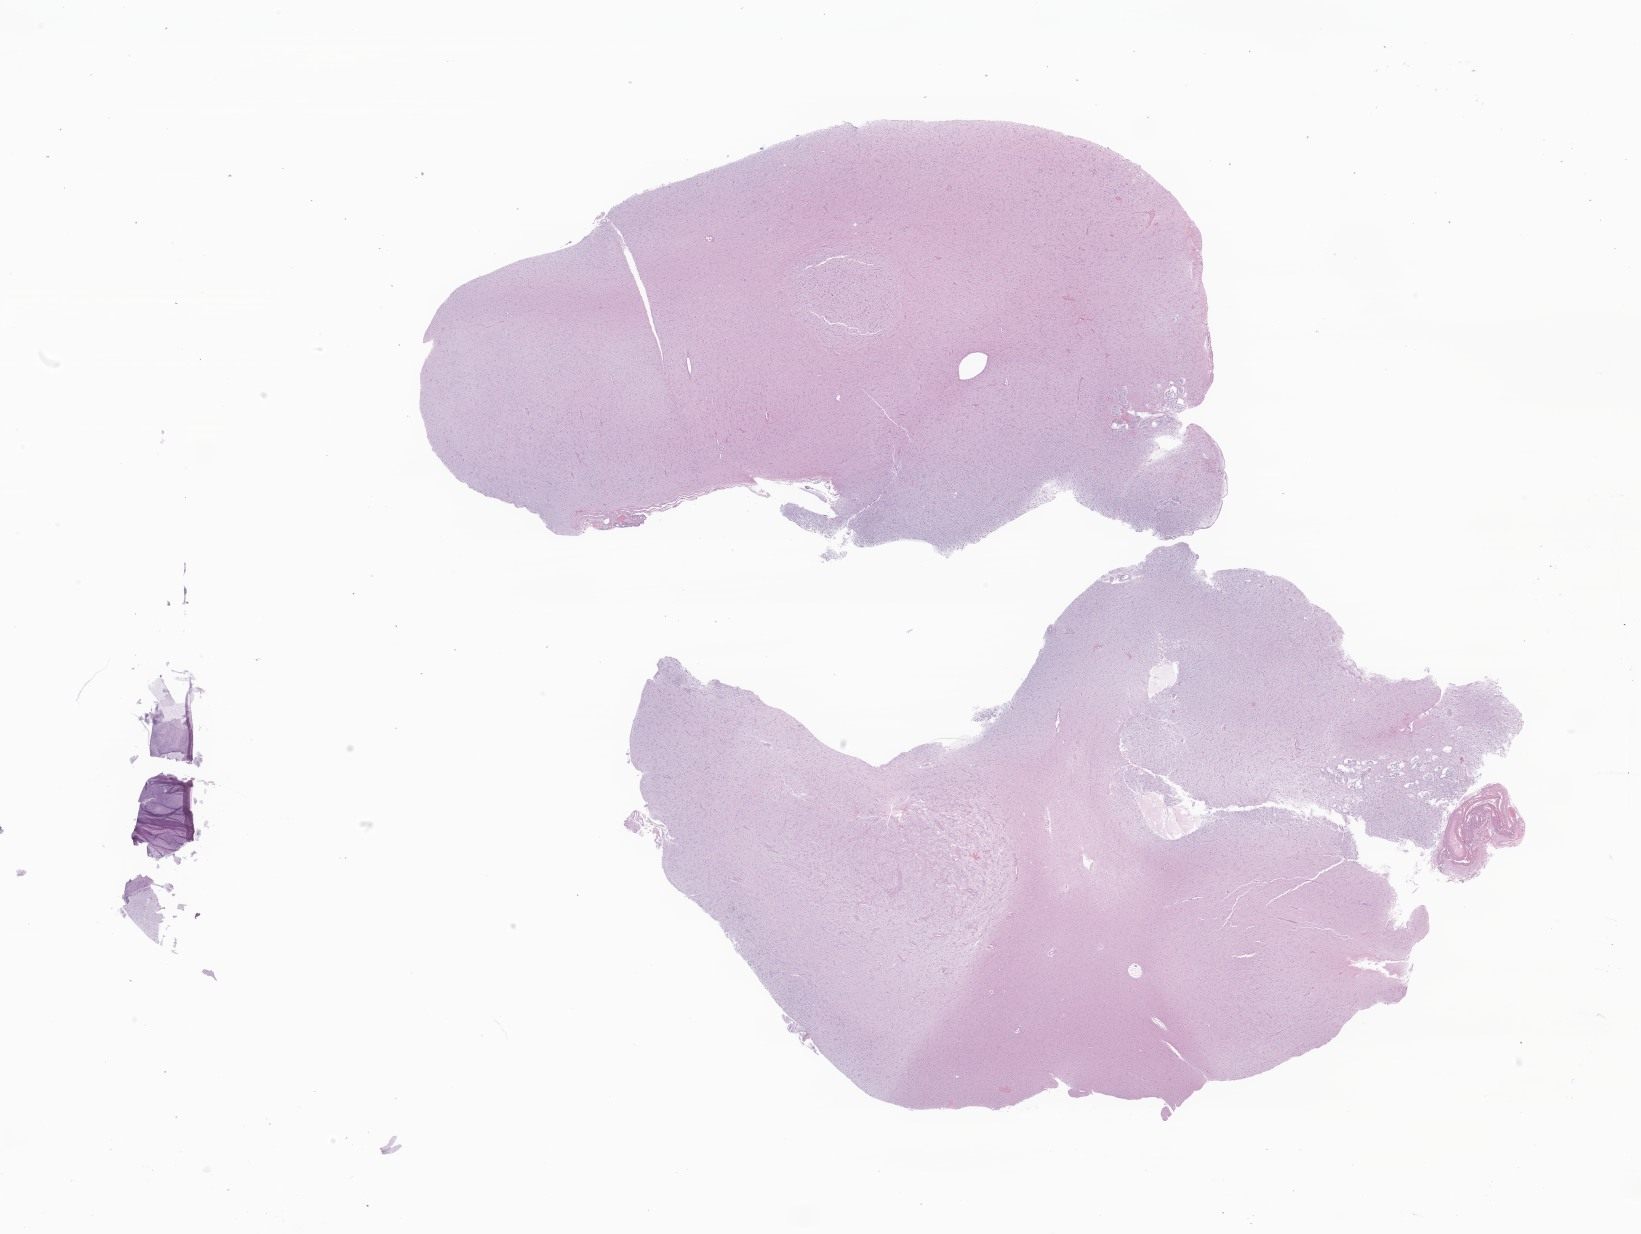
Whole-slide image, hematoxylin and eosin (H&E) stain of tumor tissue from the frontal lobe — low-resolution overview of the scanned area, about 27.7 x 20.8 mm; FFPE section. Patient: female, age 203 months (16 years 11 months).
• recorded diagnosis: Dysembryoplastic neuroepithelial tumor